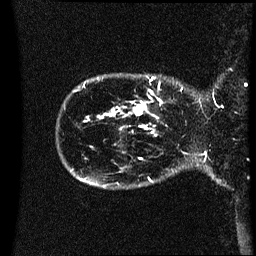
Breast MRI (dynamic contrast-enhanced), one sagittal slice. Position 5 of 60 along the scan axis. Dynamic contrast-enhanced series, image 2 of 3 at this slice position (ordered by acquisition). 1.5 T. TE 4.2 ms, TR 8.4 ms. 256 × 256 image matrix. Patient: female, 41 years. From the clinical record (not read from this slice): setting: breast cancer imaged before/during neoadjuvant chemotherapy; receptor status: HER2-positive.
Outlined on this slice (semi-automatically segmented with operator editing):
- analysis volume of interest (the breast-tissue region the enhancement analysis was run in; not a lesion): bounding box <122,80,196,119> (left, top, right, bottom; pixels)
- tumour enhancement mask (voxels above the 70 % enhancement threshold inside the analysis volume of interest): <132,90,164,119>